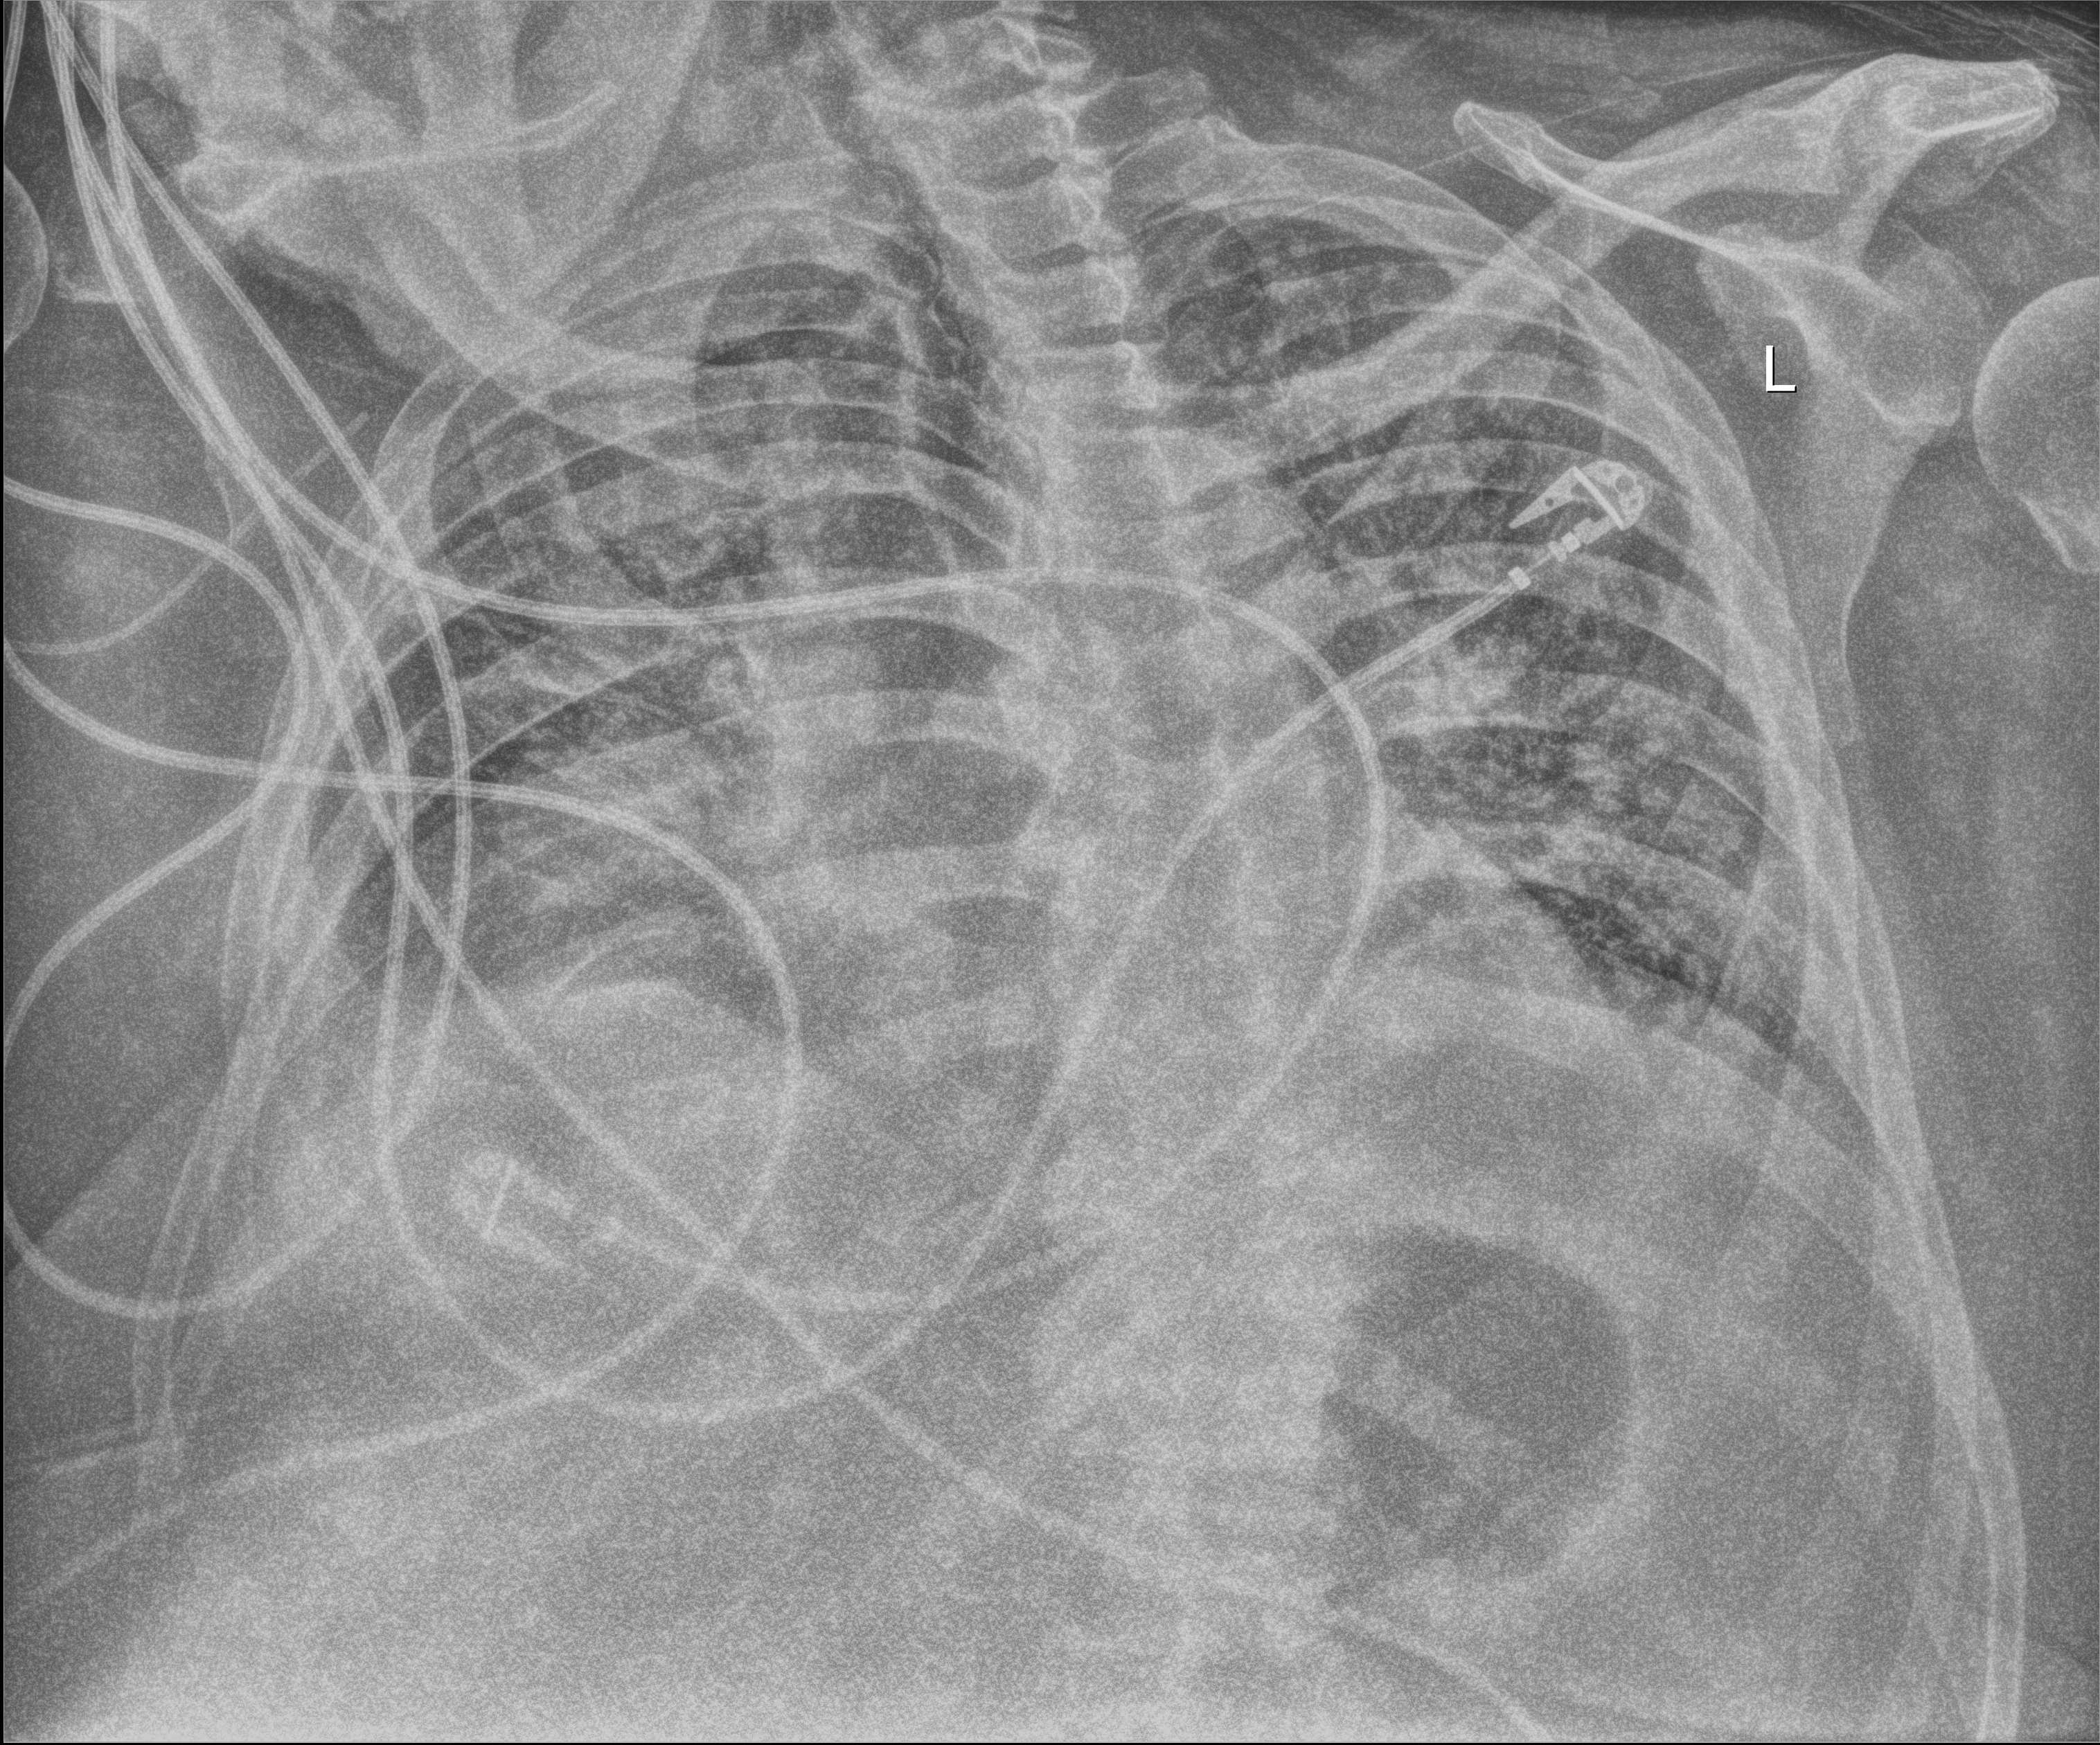
Bedside chest radiograph (digital radiography); anteroposterior (AP) projection. Patient hospitalised with COVID-19; male, aged 60–74 years.
Hospital-stay facts (about this admission, not read from this image; timing relative to this image not recorded): hypertension (admission record): yes; diabetes (admission record): yes.